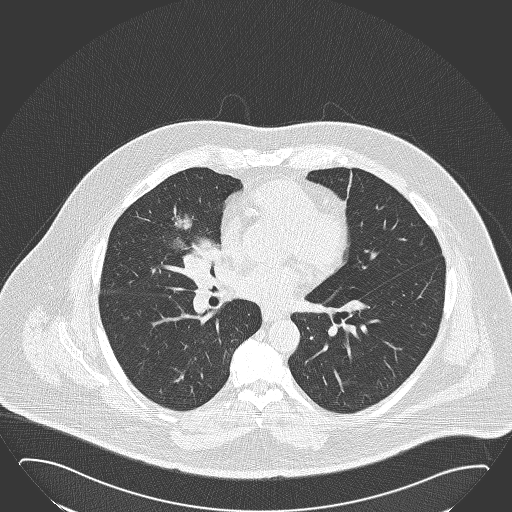
Low-dose screening chest CT, one axial slice. Slice 80 of 168 in the series (ordered by position). Reconstruction kernel B50f. 120 kVp. Lung window (W 1500 / L -600 HU). 2 mm slice thickness. 512 × 512 image matrix, field of view 432 × 432 mm.
Outlined on this slice (outlined manually by an expert reader):
- lesion 1 (tumor, hilum of right lung): bounding box <172,212,219,279> (left, top, right, bottom; pixels)